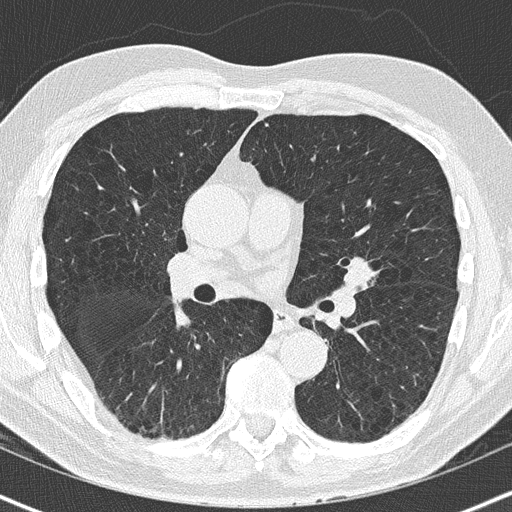
Low-dose screening chest CT, one axial slice. Slice 85 of 163 in the series (ordered by position). 120 kVp. Lung window (W 1500 / L -600 HU). 2 mm slice thickness. 512 × 512 image matrix, field of view 320 × 320 mm.
Annotated regions visible in this slice (manually delineated by an expert):
- lesion 1 (tumor, upper lobe of left lung): bounding box [x1, y1, x2, y2] px = [344, 257, 376, 283]